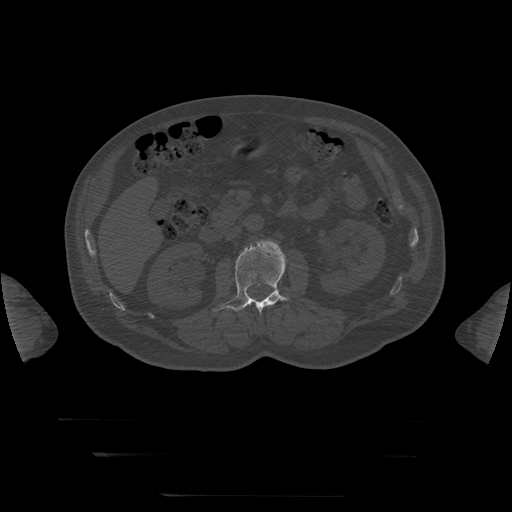
CT including the spine, one axial slice. Slice 23 of 397 in the series (ordered by position). Reconstruction kernel STANDARD. Bone window (W 1800 / L 400 HU). 512 × 512 image matrix. Patient age 73 years. From the clinical record (not read from this slice): primary cancer: prostate.
Annotated regions visible in this slice (semi-automatically segmented with operator editing):
- L1 vertebra: bounding box (x1, y1, x2, y2) in pixels: (252, 302, 267, 307)